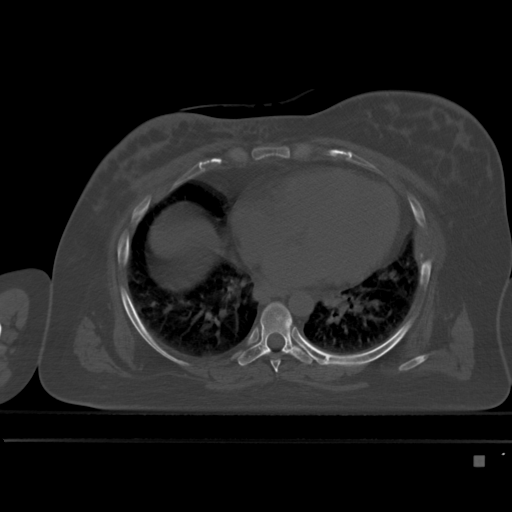
CT including the spine, one axial slice. Slice 296 of 495 in the series (ordered by position). Bone window (W 1800 / L 400 HU). 1.5 mm slice thickness. 512 × 512 image matrix, field of view 404 × 404 mm. Female patient, age 33 years. Case-level facts recorded for this patient, not image findings: primary cancer: breast; vertebrae with lytic lesions (as recorded): T1.
Outlined on this slice (semi-automatically segmented with operator editing):
- T6 vertebra: bounding box [x1, y1, x2, y2] px = [271, 360, 280, 373]
- T7 vertebra: [238, 302, 315, 366]